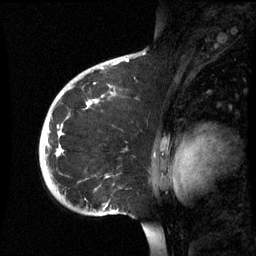
Breast MRI (dynamic contrast-enhanced), one sagittal slice. Position 42 of 60 along the scan axis. Dynamic contrast-enhanced series, image 2 of 3 at this slice position (ordered by acquisition). 1.5 T. TE 4.2 ms, TR 8.9 ms. 2.6 mm slice thickness. 256 × 256 image matrix, field of view 220 × 220 mm. Female patient, age 35 years. Case-level facts recorded for this patient, not image findings: setting: breast cancer imaged before/during neoadjuvant chemotherapy; receptor status: HR-positive, HER2-negative.
Outlined on this slice (semi-automatically segmented with operator editing):
- analysis volume of interest (the breast-tissue region the enhancement analysis was run in; not a lesion): bounding box <39,74,162,217> (left, top, right, bottom; pixels)
- tumour enhancement mask (voxels above the 70 % enhancement threshold inside the analysis volume of interest): <59,100,92,149>